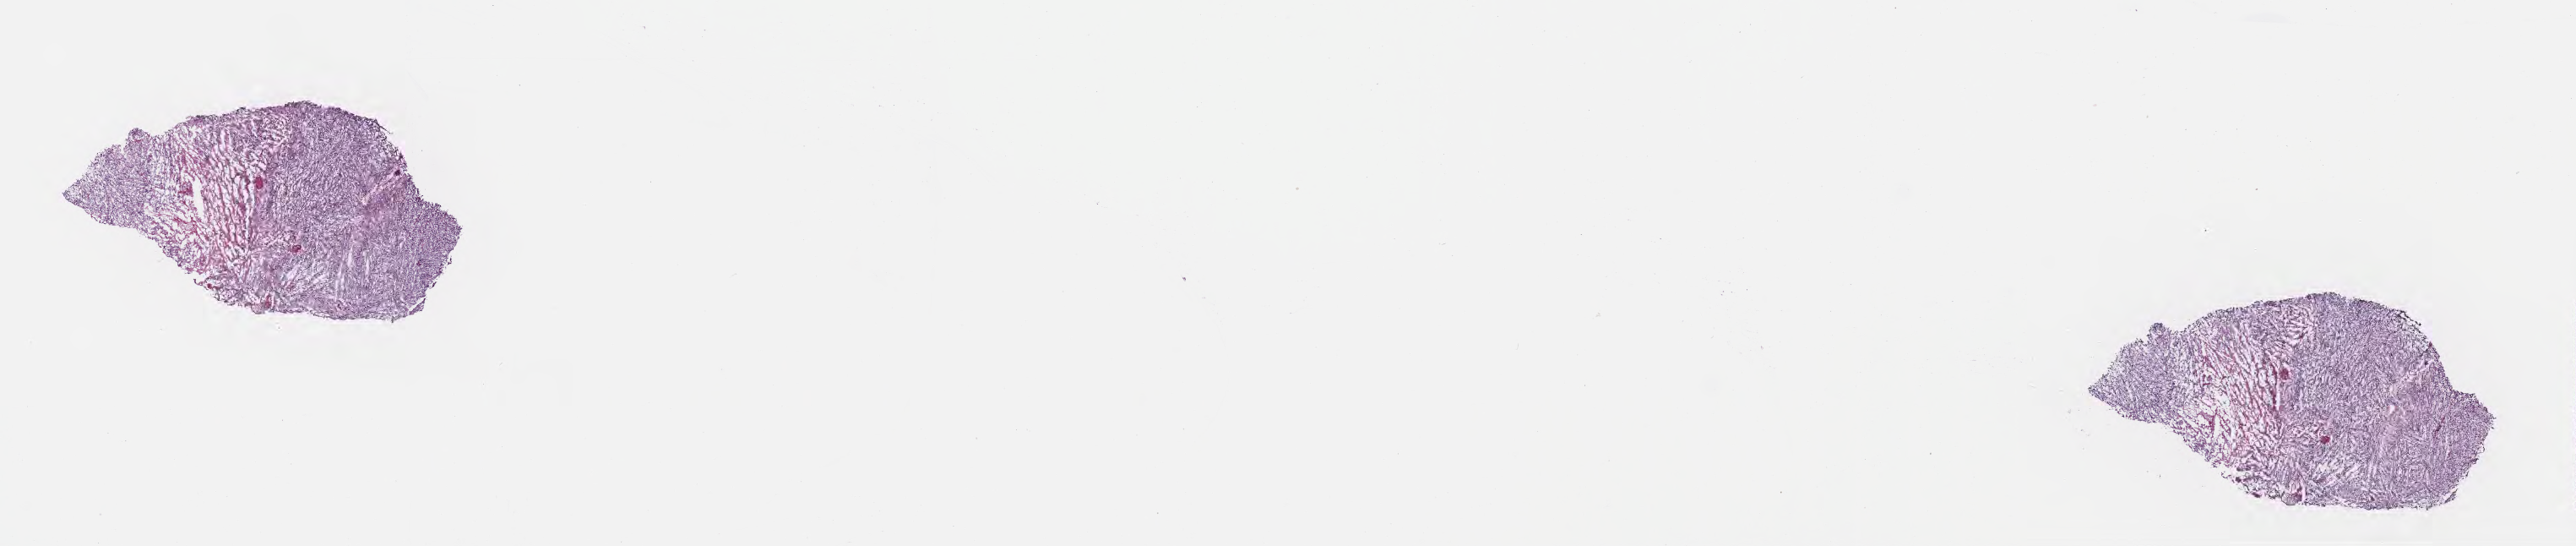
Whole-slide image, haematoxylin and eosin stain — a low-resolution overview of the entire scanned area, about 24.6 x 5.2 mm; cryosection; primary tumor; site: brain. Female patient; age at initial diagnosis 50 years. Pathologist review of this section (percent, as recorded): tumor cells 59%, tumor nuclei 84%, stromal cells 13%, necrosis 17%, normal cells 11%. Inflammatory infiltration, as recorded: lymphocyte infiltration 0%, monocyte infiltration 0%, neutrophil infiltration 0%.
Section: bottom of the tissue portion. Diagnosis: Glioblastoma, NOS.